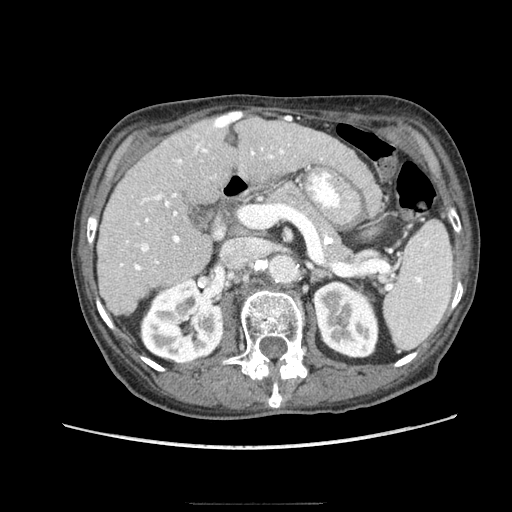
Contrast-enhanced abdominal CT (liver protocol), one axial slice. Position 43 of 83 along the scan axis. 140 kVp. Soft-tissue window (W 400 / L 40 HU). 2.5 mm slice thickness. 512 × 512 image matrix, field of view 360 × 360 mm. From the clinical record (not read from this slice): diagnosis: hepatocellular carcinoma (patient treated with transarterial chemoembolisation; whether this scan precedes or follows treatment is not stated here); TNM stage (as recorded): Stage-I; Child-Pugh class: A; tumour differentiation: moderately differentiated; tumour nodularity: uninodular.
Outlined on this slice (semi-automatically segmented with operator editing):
- liver parenchyma outside the tumour (the mass and vessels are separate outlines, so this box may not span the whole liver): box from (x=96, y=113) to (x=343, y=314) px
- liver vessels: (x=120, y=113)–(x=291, y=270)